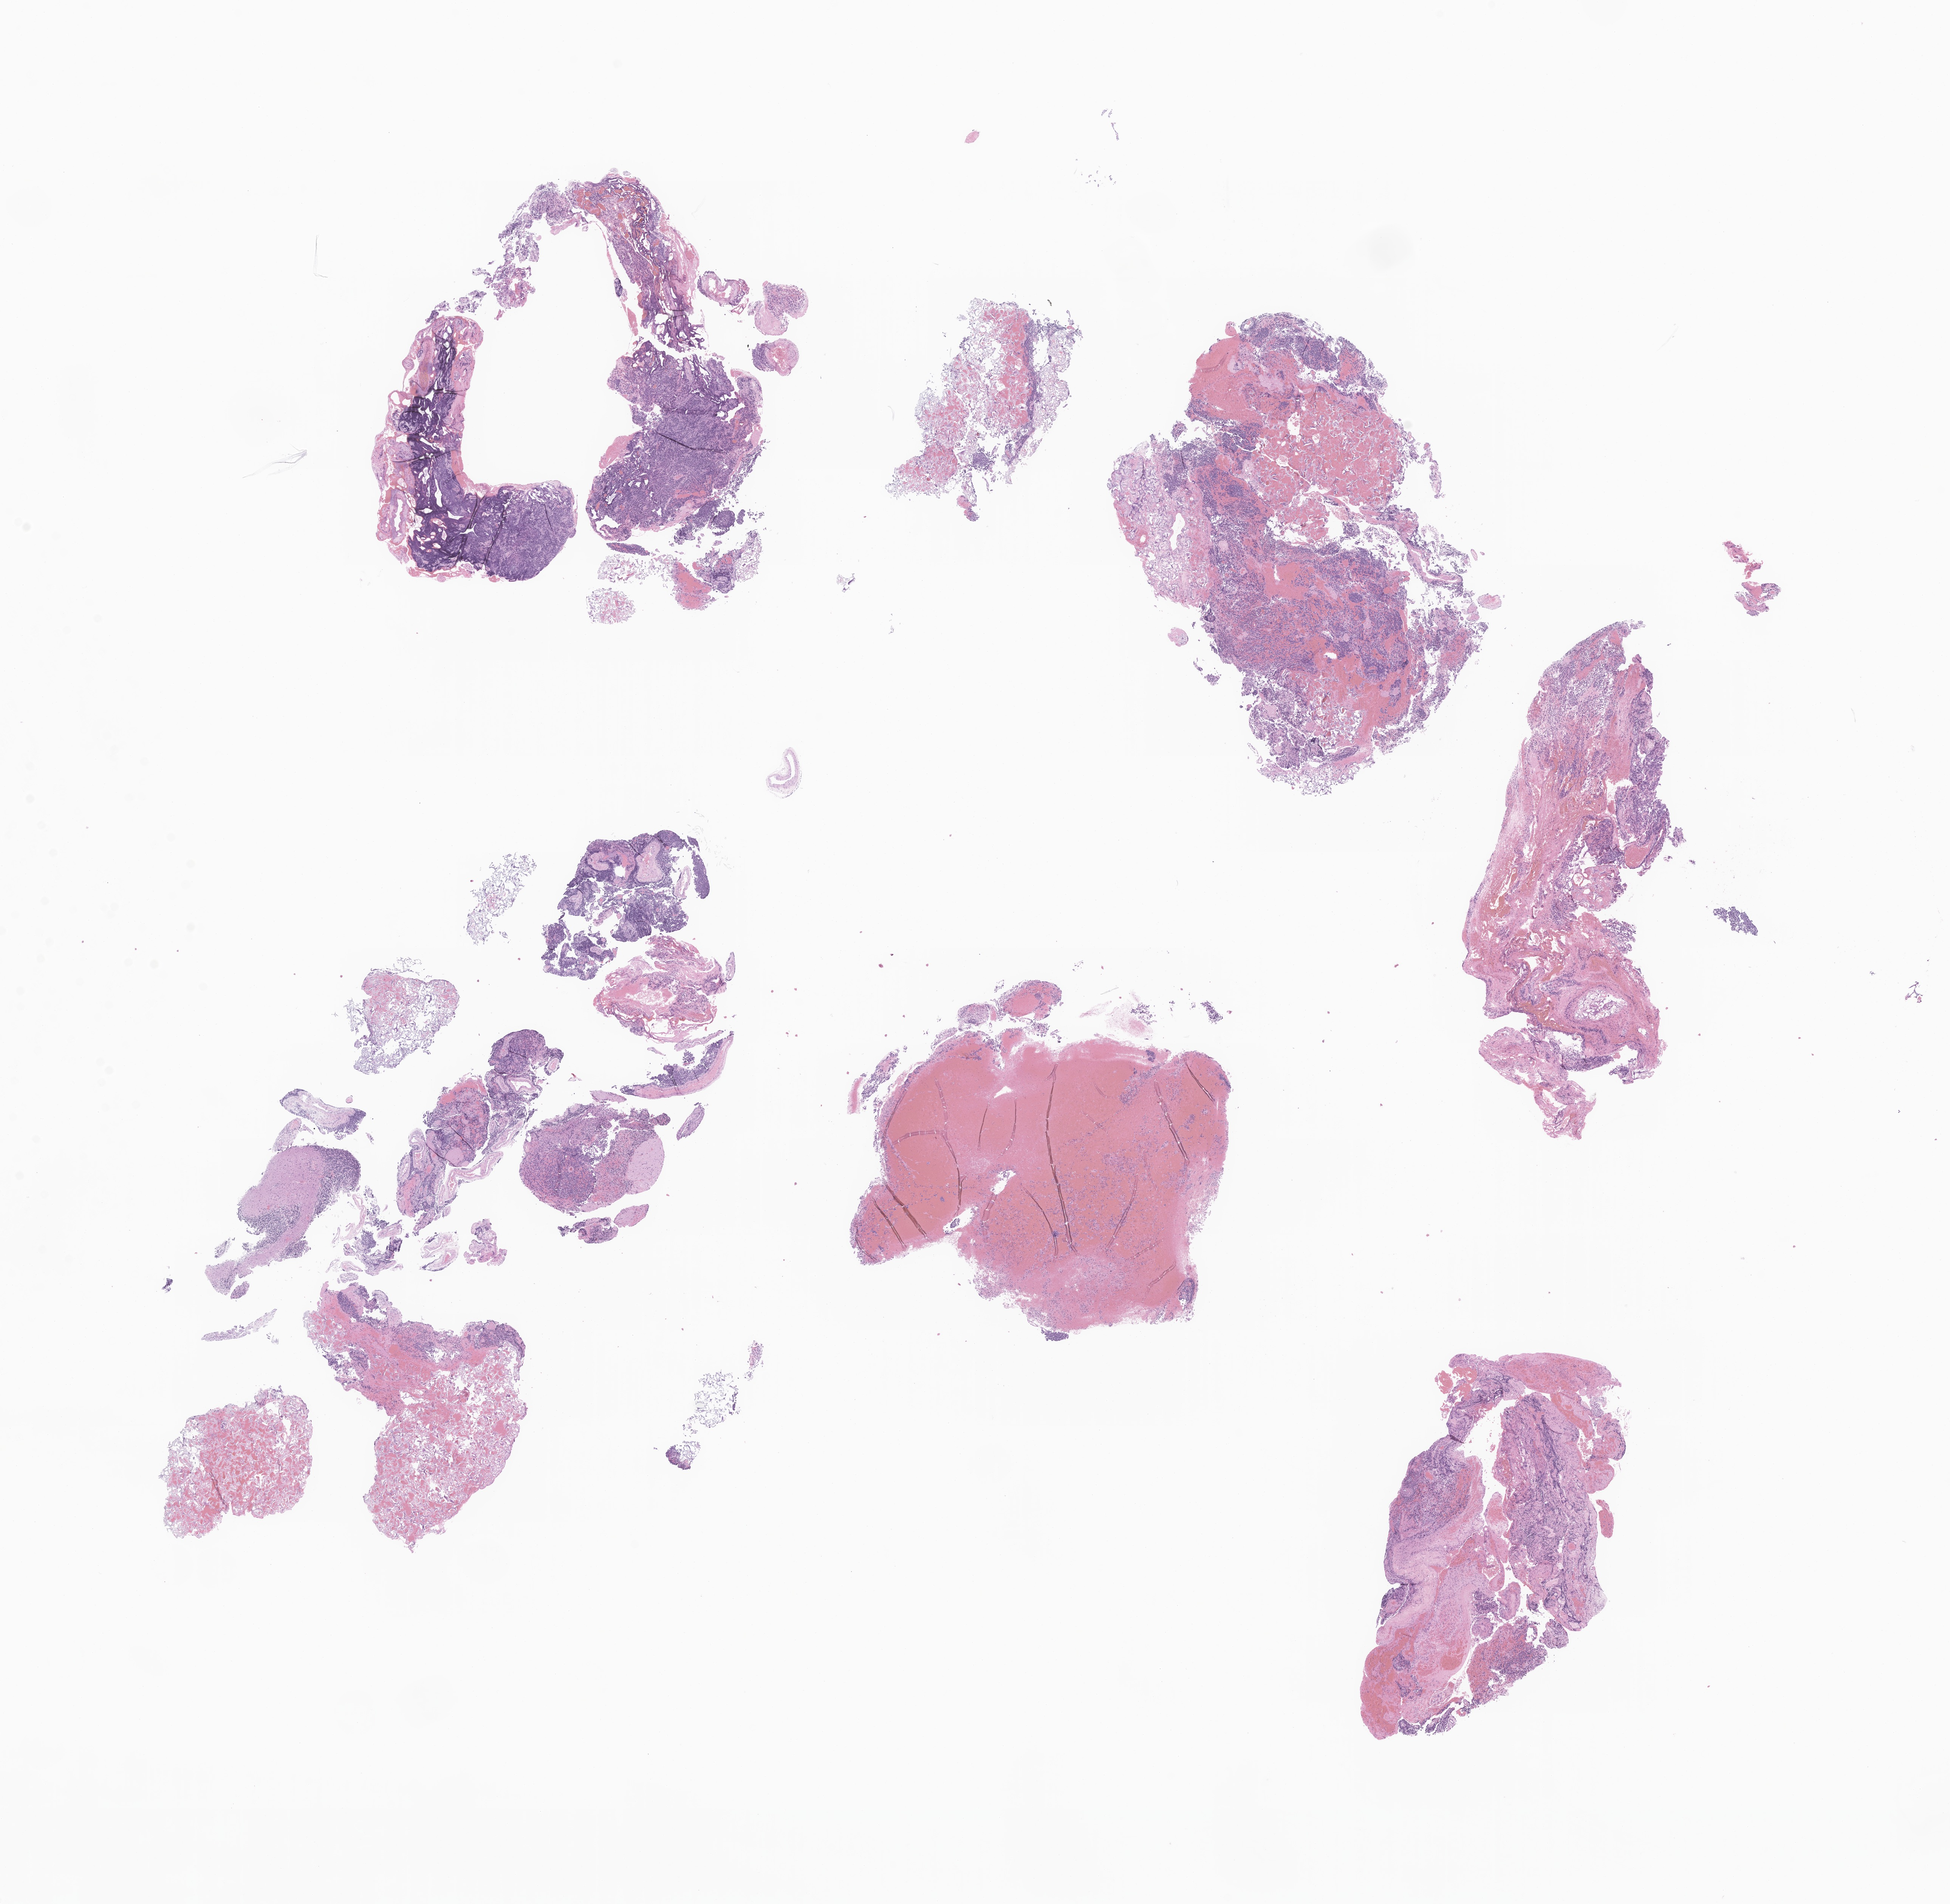
Whole-slide image, hematoxylin and eosin (H&E) stain of tumor tissue from the cerebellum — shown as a low-resolution overview of the whole scanned area (about 21.8 x 21.2 mm), formalin-fixed, paraffin-embedded (FFPE) tissue. Male patient, age 176 months.
- recorded diagnosis: Medulloblastoma, NOS